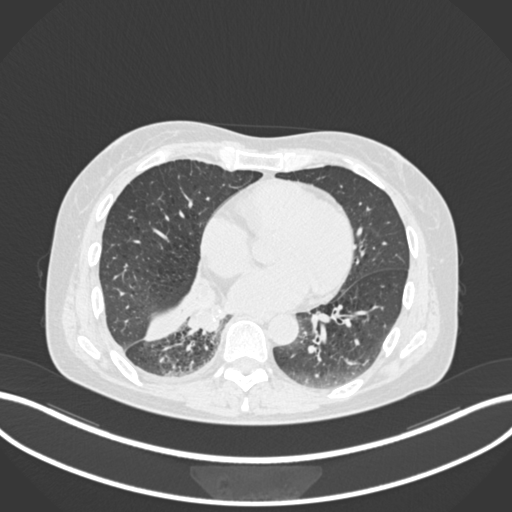
Chest CT, one axial slice. Position 62 of 168 along the scan axis. Reconstruction kernel B30f. Lung window (W 1500 / L -600 HU). 512 × 512 image matrix. Female patient, age 63 years. Case-level facts recorded for this patient, not image findings: clinical TNM (as recorded): T1c N0 M0.
Outlined on this slice (bounding box drawn by a radiologist):
- lung tumour (recorded histology: adenocarcinoma): bounding box (x1, y1, x2, y2) in pixels: (184, 305, 230, 336)